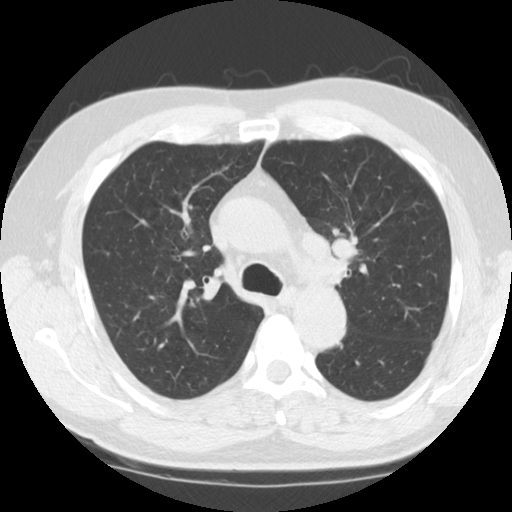
Axial slice from a low-dose chest CT screening exam; third screening round (two years after baseline); lung window (W 1500 / L -600 HU); slice 38 of 124 in the series. Male, age 60 years at enrolment. Current smoker at enrolment.
Expert-annotated lung lesion, bounding box <315,222,369,275> (left, top, right, bottom; pixels). Reader record for this screening exam (exam-level; its link to the box is not recorded): non-calcified nodule or mass ≥4 mm, left upper lobe, 24 × 21 mm, smooth margins, soft tissue attenuation, pre-existing on the prior screen: no. Later outcome: lung cancer diagnosed 14 days after this screen — small cell carcinoma, NOS, left upper lobe, stage IIA (AJCC 6th edition), 26 mm at pathology.